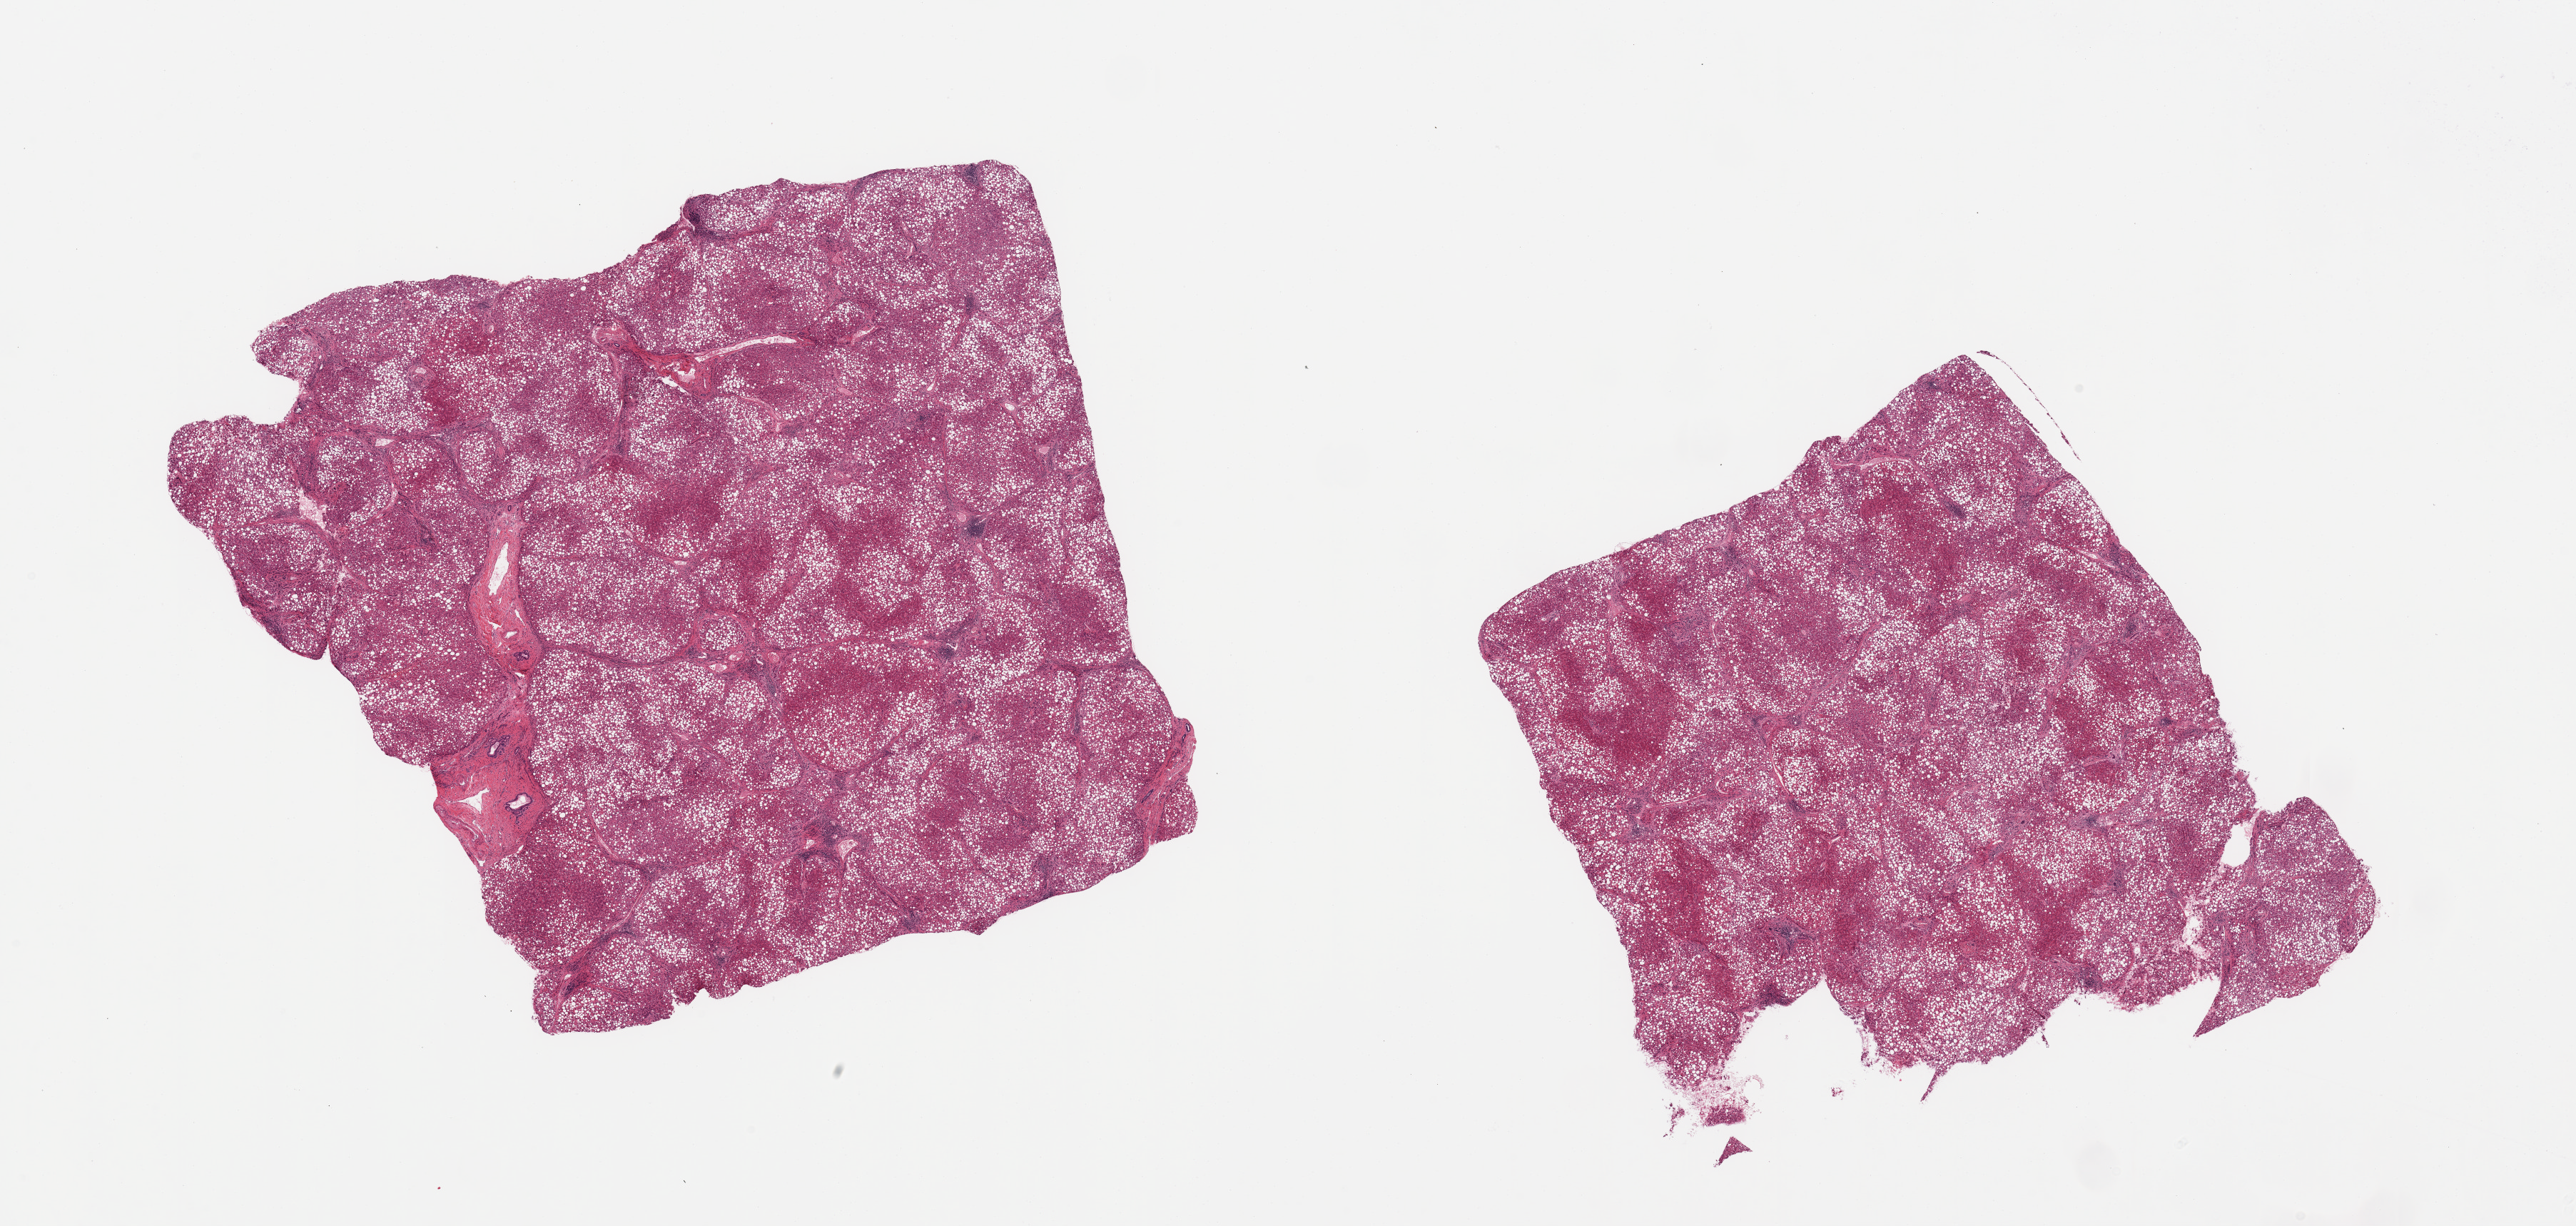
Whole-slide image, haematoxylin and eosin stain — whole scanned area (about 28.5 x 13.6 mm) shown as a low-resolution overview; PAXgene-fixed paraffin-embedded (PFPE) section; section of liver (target tissue); tissue donor sample. Female donor.
Reviewer comment on this tissue sample: 2 pieces; 80% macrovesicular steatosis, portal inflammation and bridging fibrosis consistent with nonalcoholic steatohepatitis.